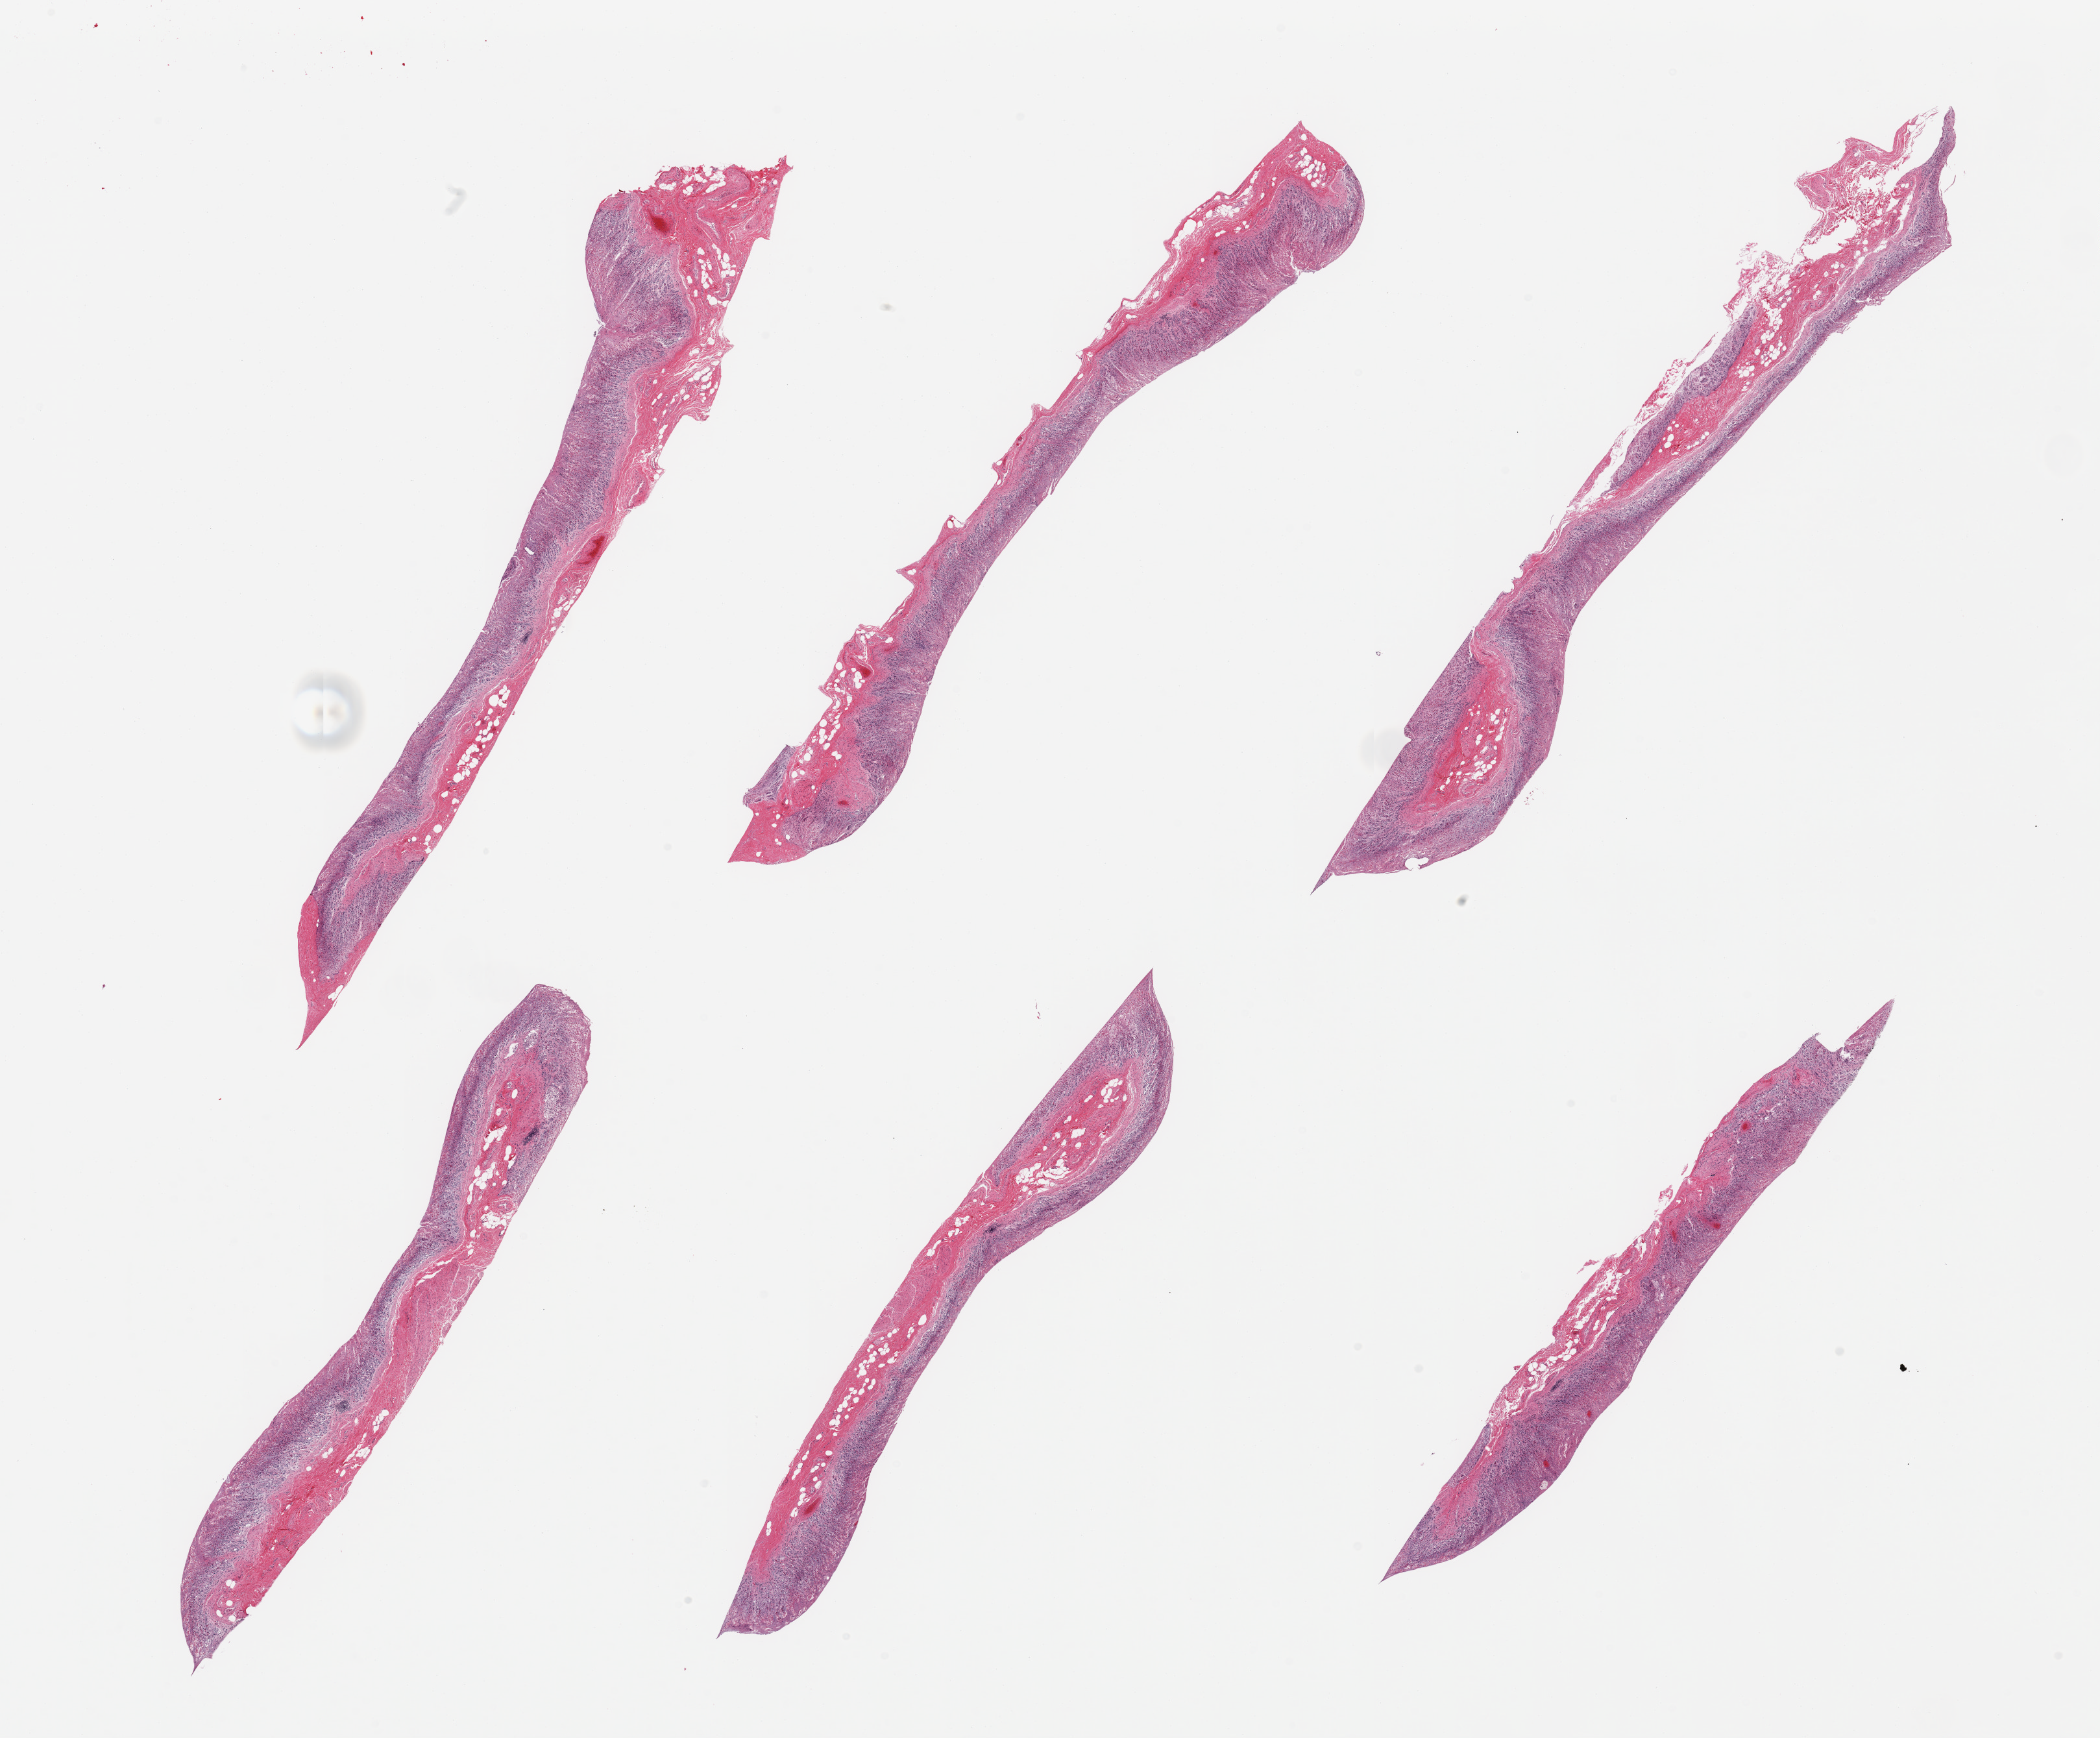
H&E whole-slide image — whole scanned area (about 25.6 x 21.2 mm, acquisition: 20x scan) shown as a low-resolution overview, PAXgene-fixed, paraffin-embedded tissue, target tissue: stomach, tissue donor sample. Donor sex: male.
Pathologist's review note for this sample: 6 pieces; predominantly autolyzed mucosa.